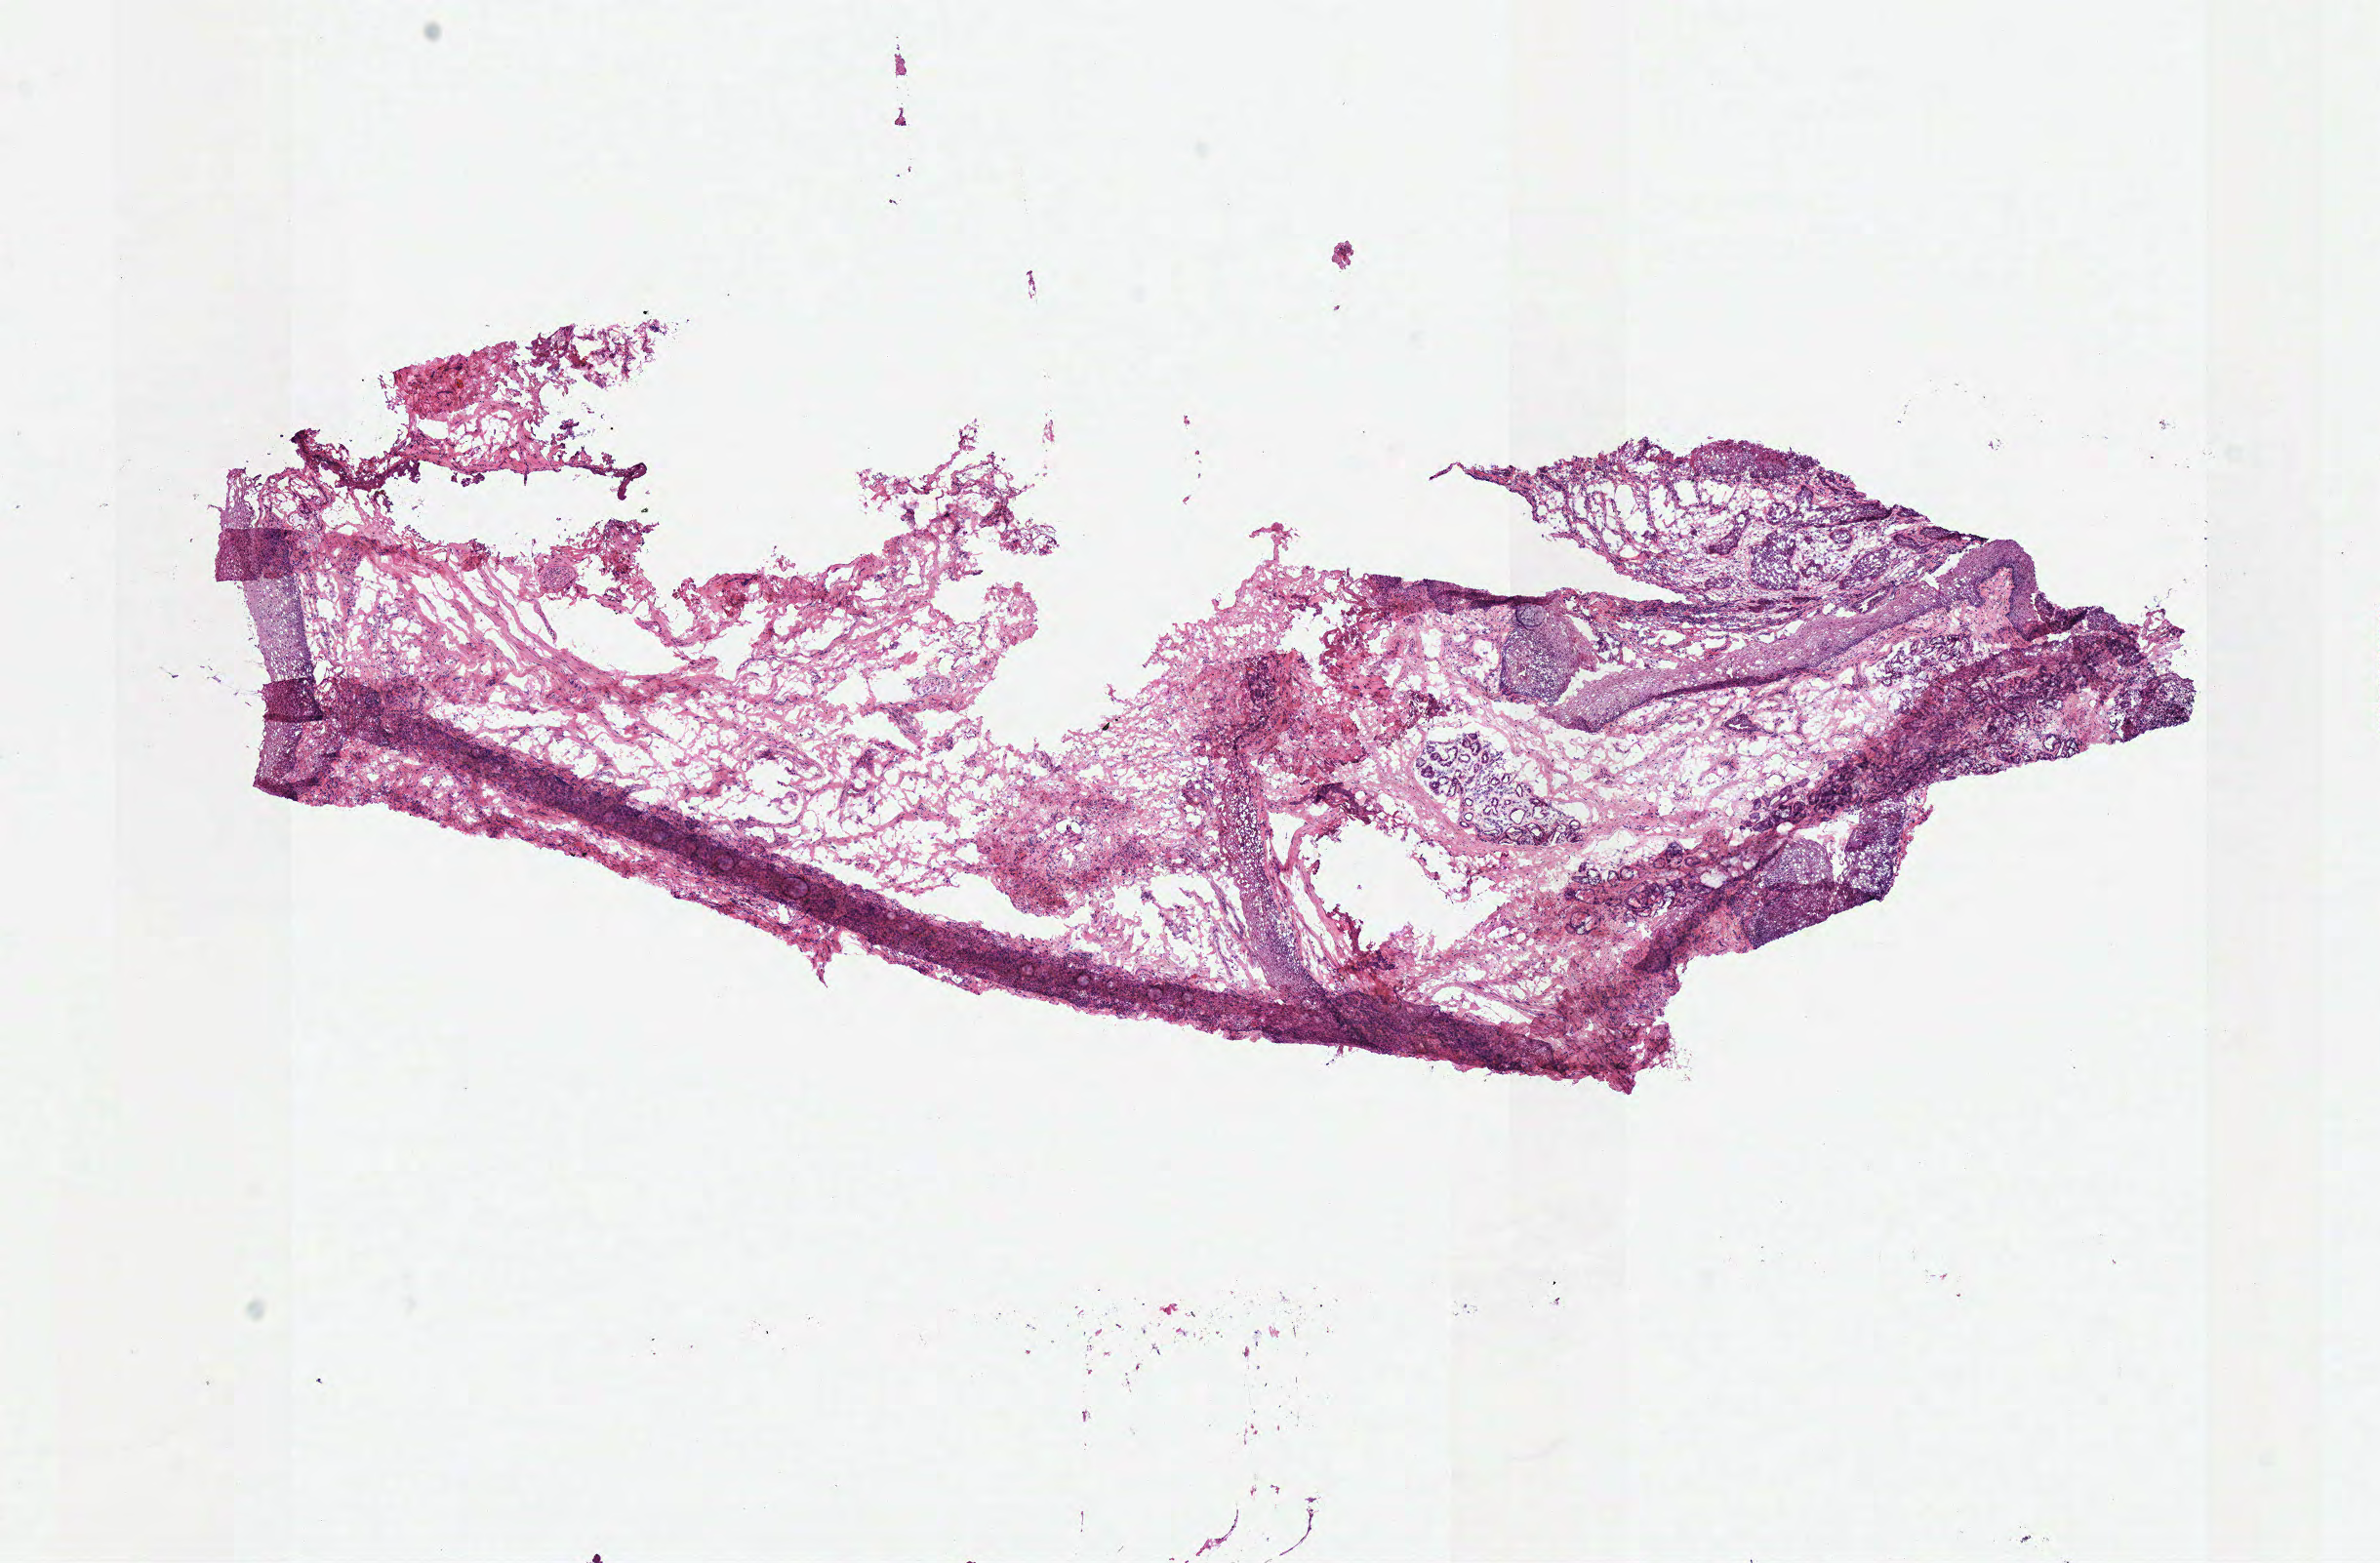
Digitized H&E tissue section (whole slide), a low-resolution overview of the entire scanned area, about 9.6 x 6.3 mm (acquisition: 40x scan); frozen section from the top of the tissue portion; head and neck, solid tissue normal (non-tumour tissue) sample. Patient: male, age at initial diagnosis 67 years.
This section: solid tissue normal (non-tumour) sample from the same patient. Patient diagnosis: Squamous cell carcinoma, NOS (larynx, NOS).